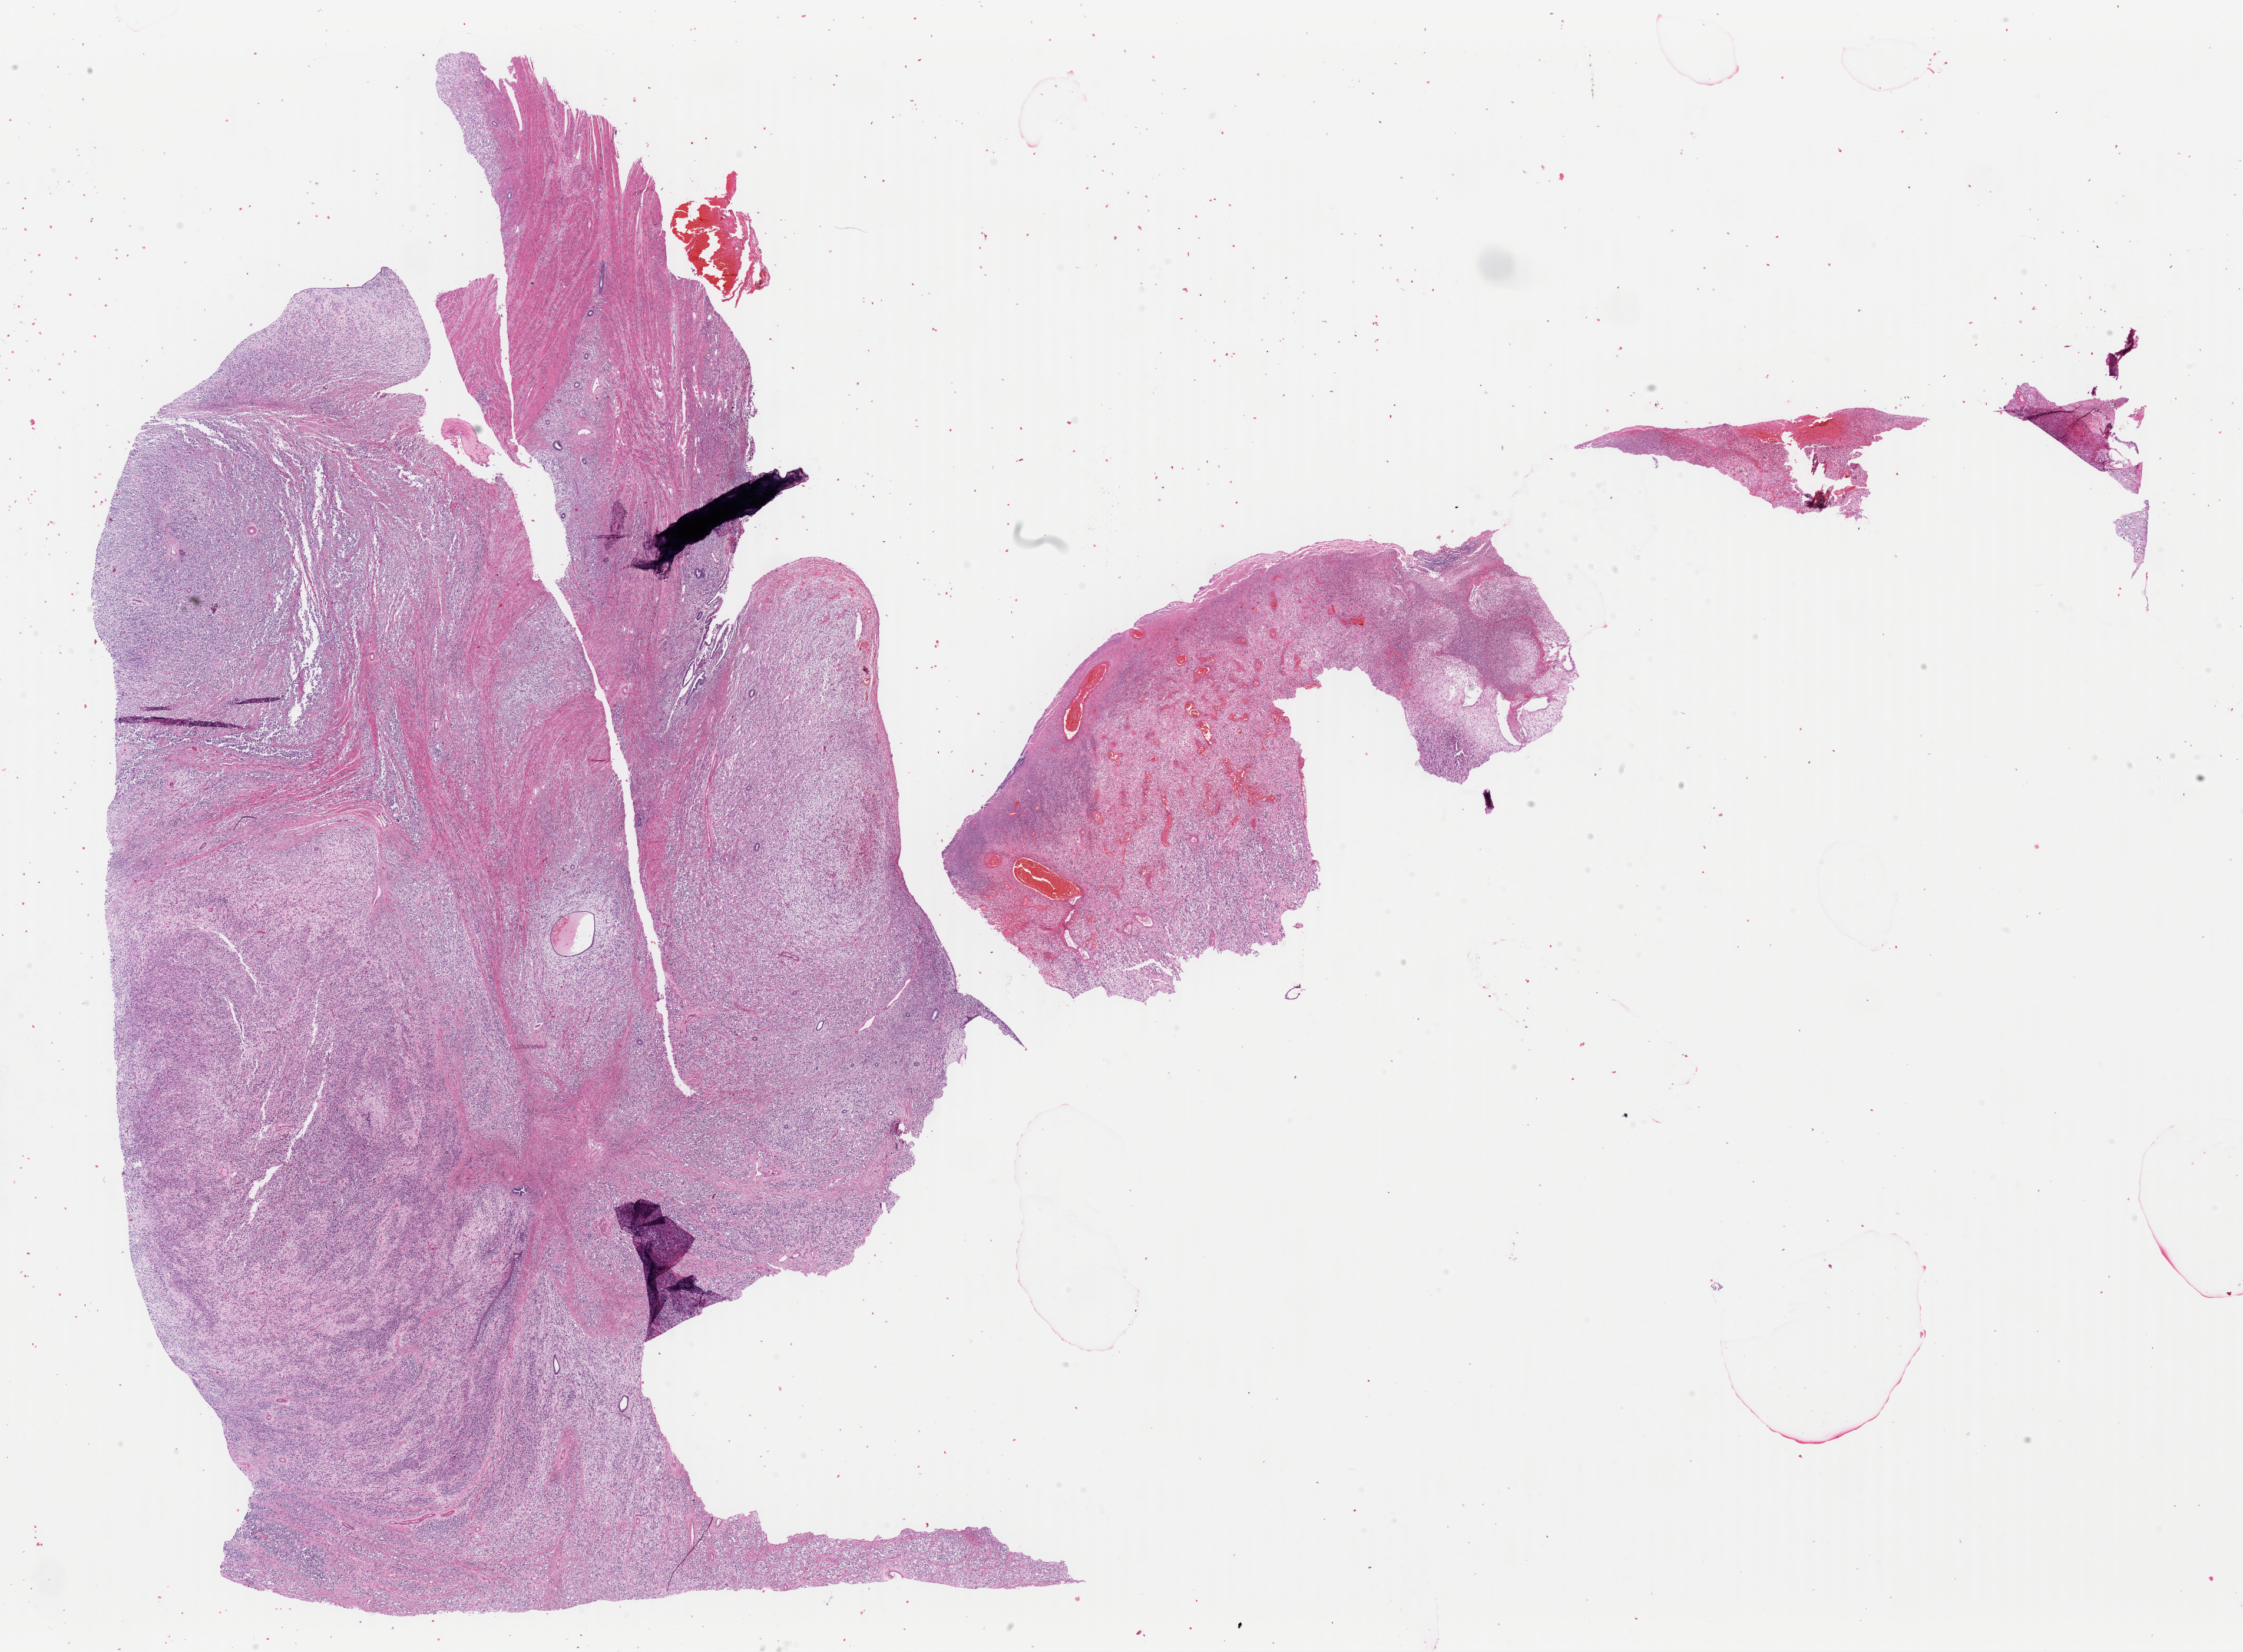
Whole-slide histology image, H&E, a low-resolution overview of the entire scanned area, about 30.1 x 22.2 mm, formalin-fixed paraffin-embedded (FFPE) diagnostic section, sample: primary tumour, uterus. Female, age 60 years at initial diagnosis.
Diagnosis: Carcinosarcoma, NOS. FIGO stage: IVB.